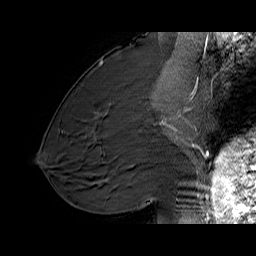
Breast MRI (dynamic contrast-enhanced), one sagittal slice; slice 29 of 60 in the series (ordered by position); dynamic contrast-enhanced series, time point 2 of 6 at this slice position (early post-contrast); 1.5 T; TE 6.1 ms, TR 32.9 ms; 256 × 256 image matrix, field of view 220 × 220 mm. Female patient. From the clinical record (not read from this slice): setting: breast cancer imaged before/during neoadjuvant chemotherapy; receptor status: HER2-positive.
Annotated regions visible in this slice (semi-automatically segmented with operator editing):
- analysis volume of interest (the breast-tissue region the enhancement analysis was run in; not a lesion): bounding box <127,95,194,165> (left, top, right, bottom; pixels)
- tumour enhancement mask (voxels above the 100 % enhancement threshold inside the analysis volume of interest): <161,115,180,131>